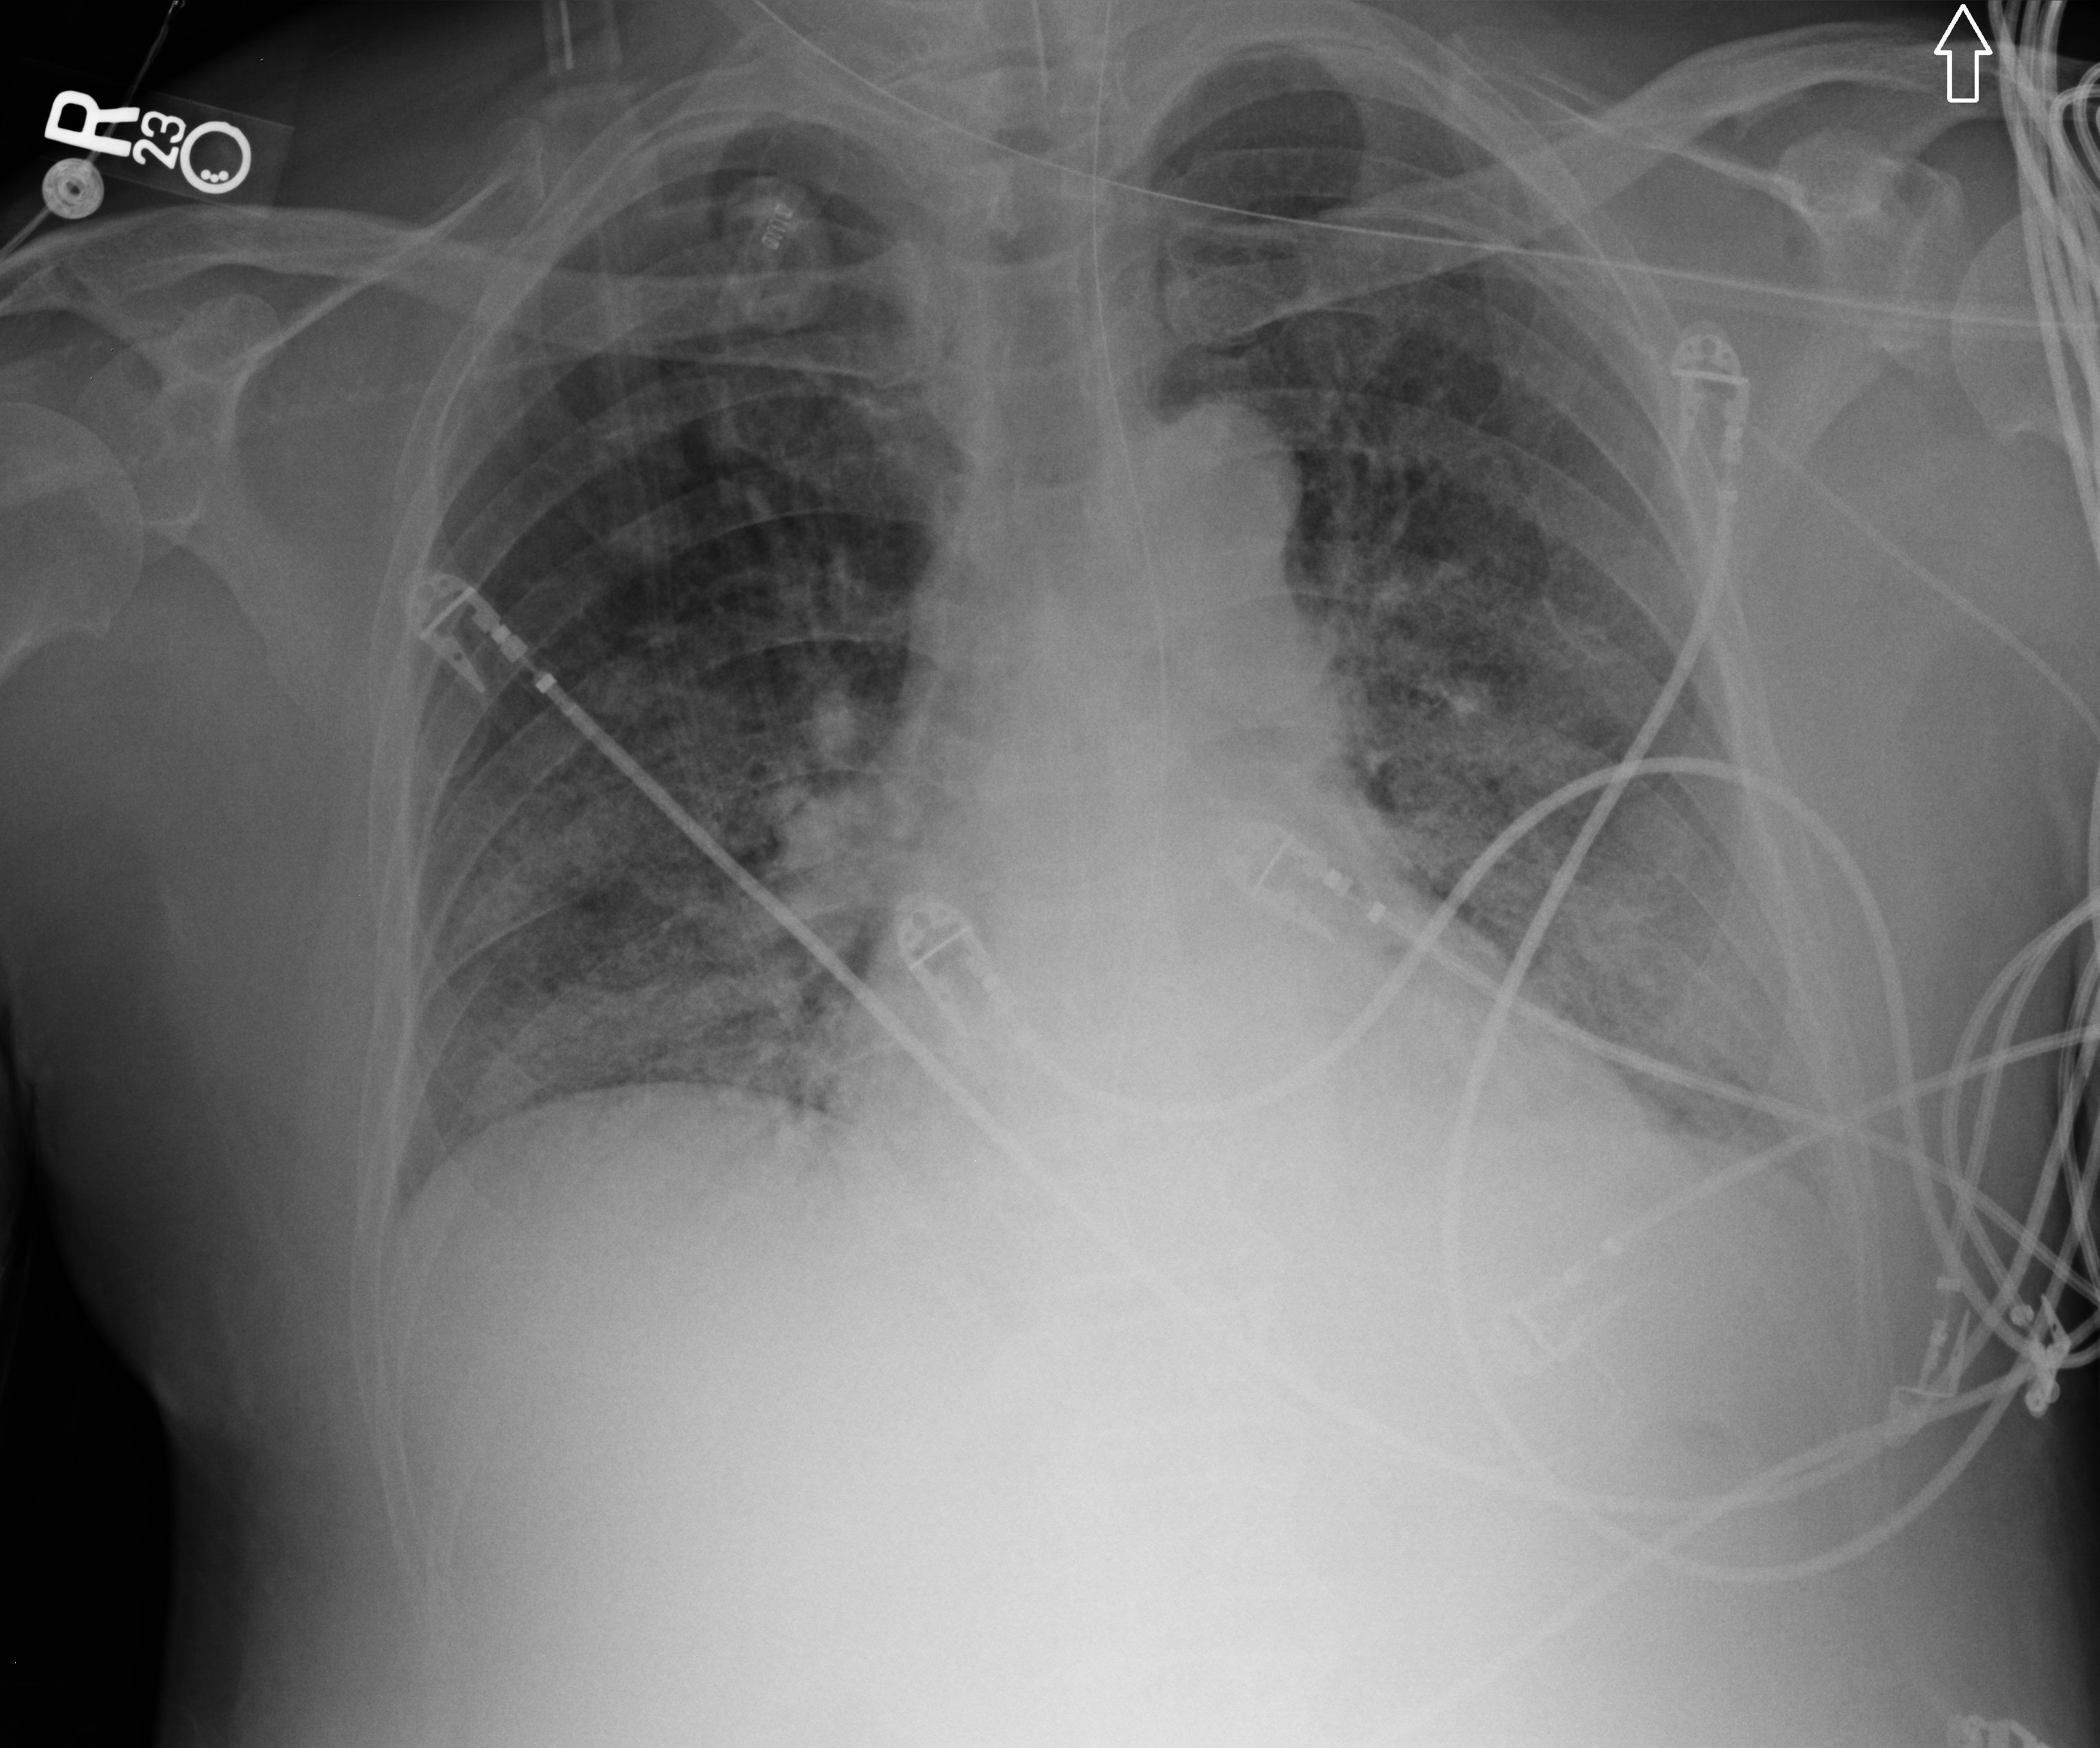
Bedside chest radiograph (computed radiography); anteroposterior (AP) projection. Male patient hospitalised with COVID-19, age 60–74 years.
From the hospital-stay record, not from the radiograph (when in the stay this image was taken is not recorded):
- admitted to intensive care during this hospital stay: yes
- diabetes (admission record): yes